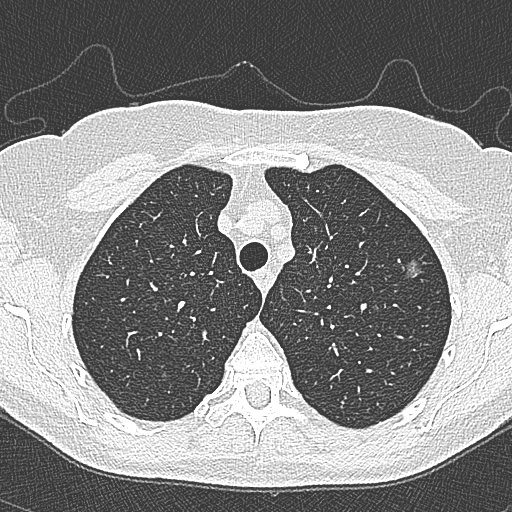
Chest CT (low-dose screening protocol), one axial image; second screening round (one year after baseline); lung window (W 1500 / L -600 HU); 120 kVp; 512 × 512 image matrix. Female, age 65 years at enrolment. Current smoker at enrolment.
Expert-annotated lung lesion, bounding box <395,251,432,286> (left, top, right, bottom; pixels). The screening reader recorded 4 non-calcified nodules or masses ≥4 mm on this exam (left upper lobe, left upper lobe, left upper lobe, right lower lobe); which of them this box marks is not recorded. Lung cancer was diagnosed 54 days after this screen: bronchiolo-alveolar carcinoma, non-mucinous, left upper lobe, stage IA (AJCC 6th edition), 10 mm at pathology.